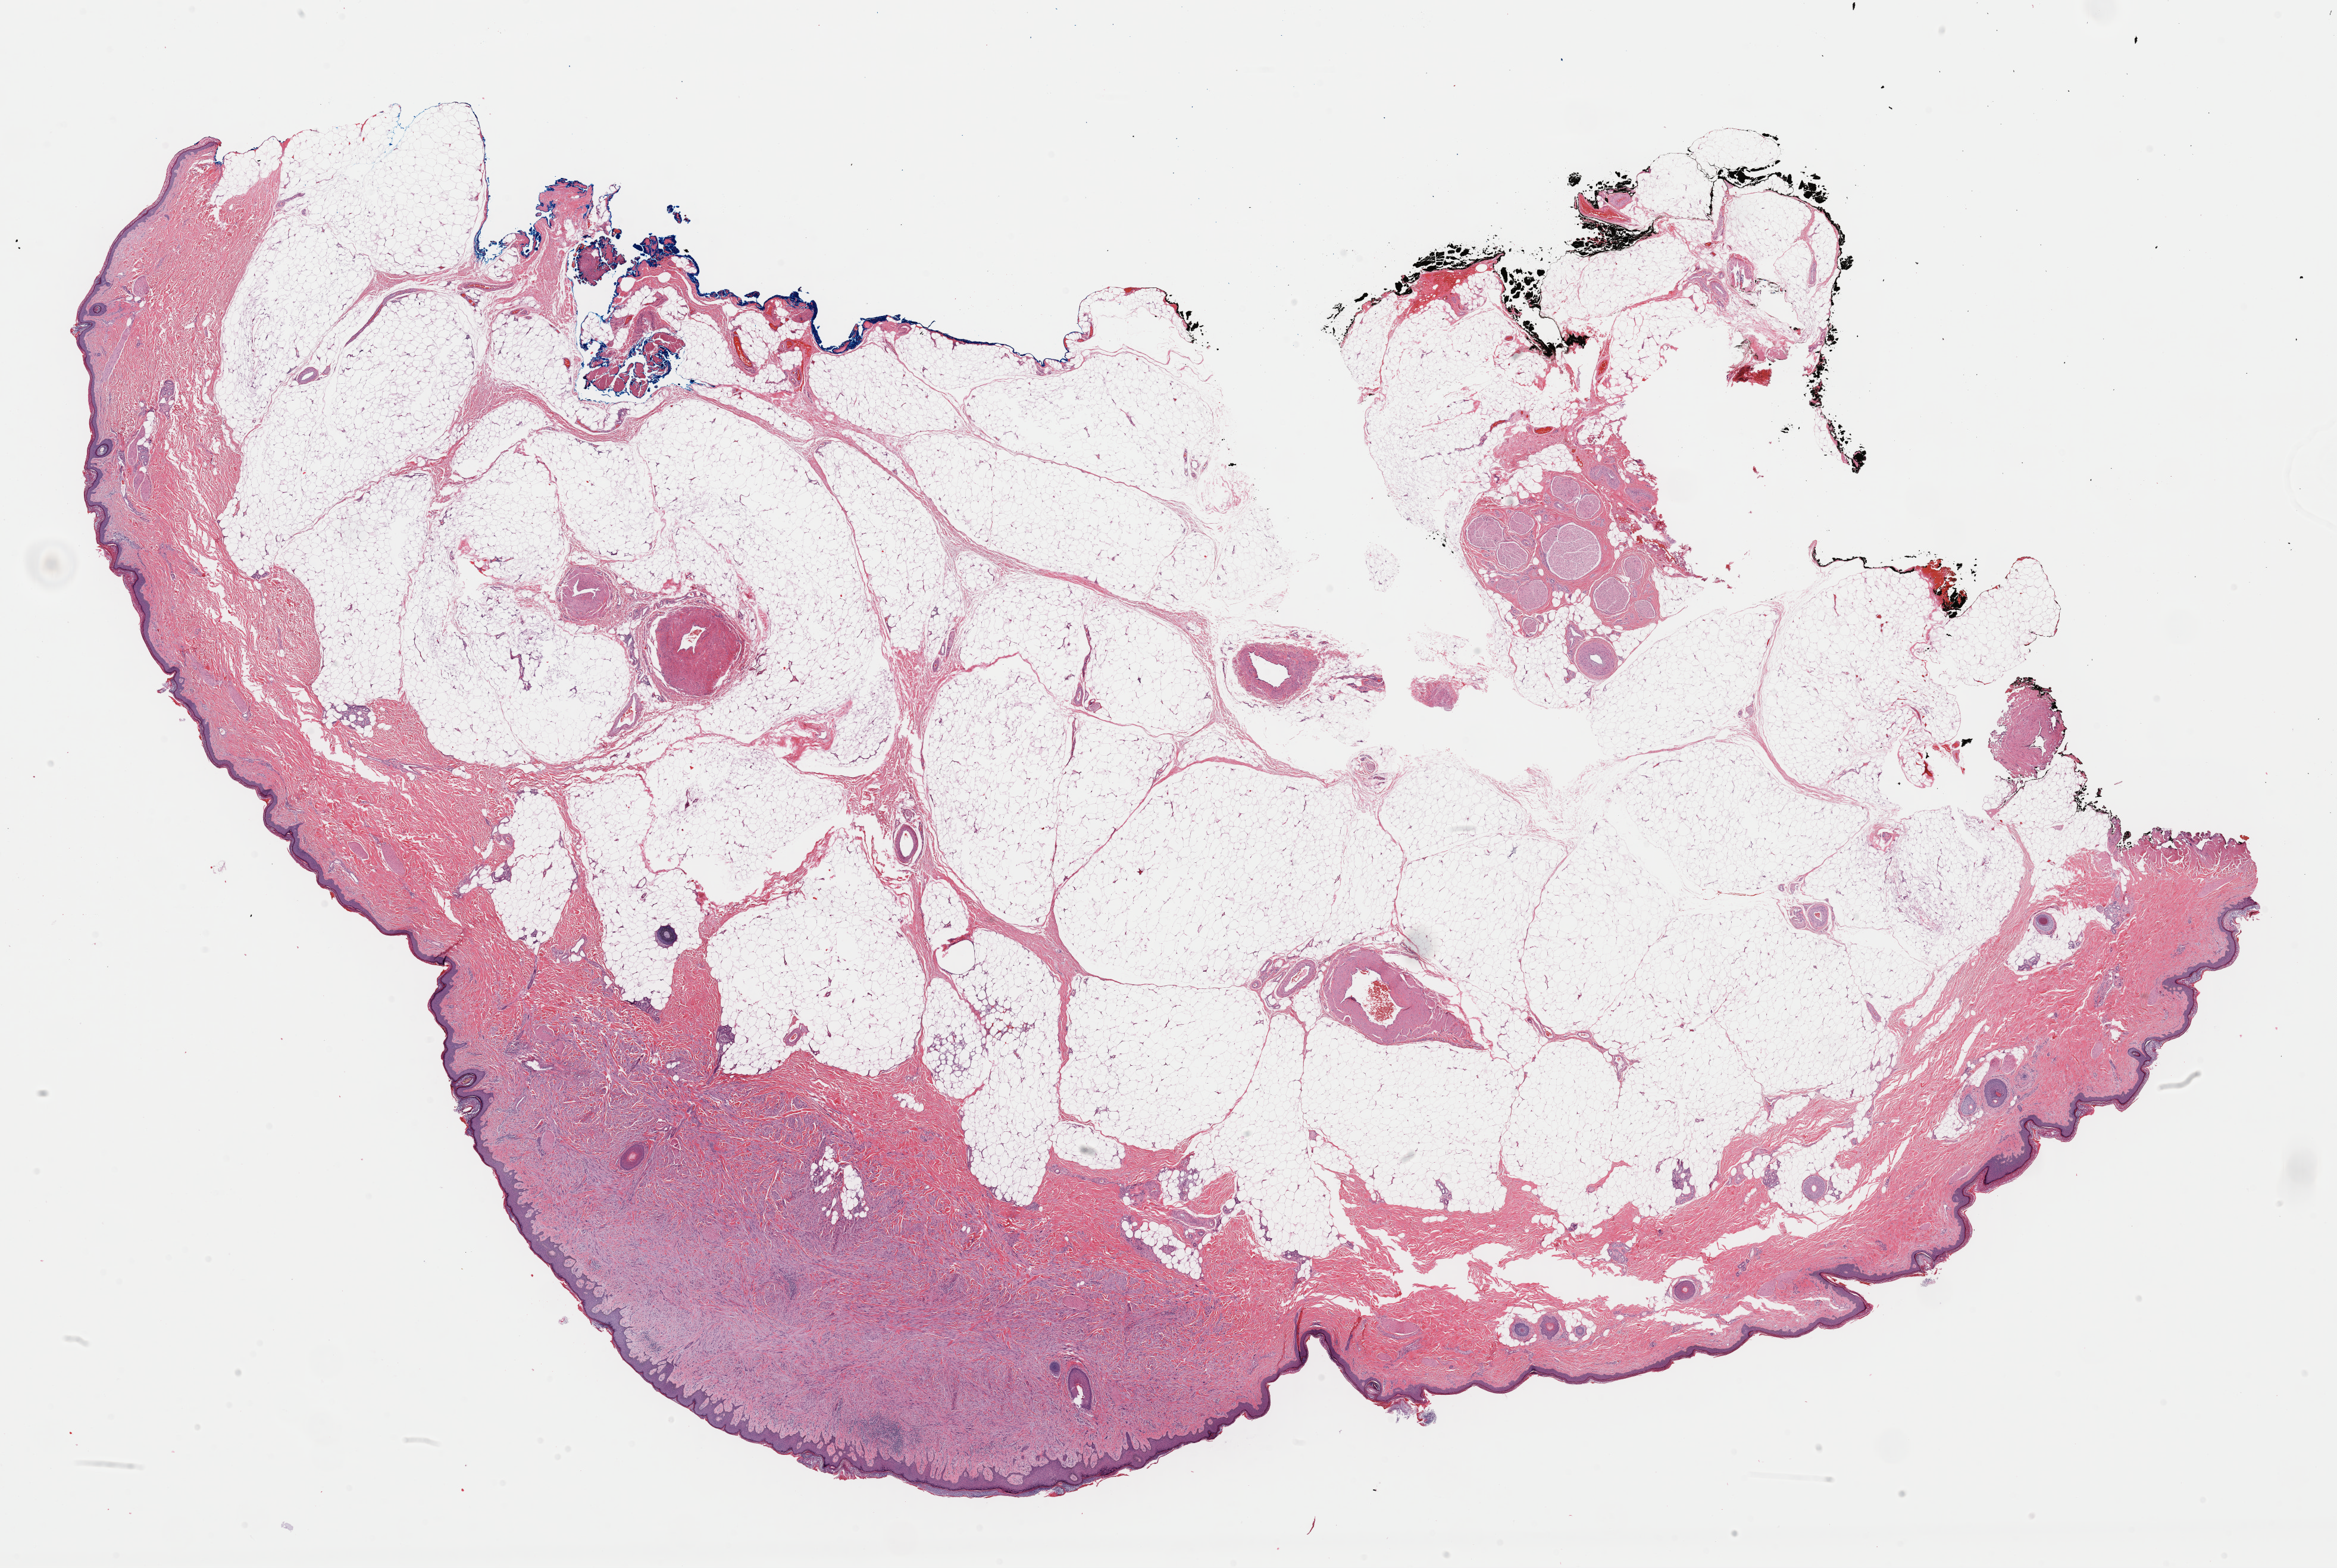
Digitized H&E tissue section (whole slide), a low-resolution overview of the entire scanned area, about 31.0 x 20.8 mm (slide scanned at 40x), formalin-fixed paraffin-embedded (FFPE) diagnostic section, primary tumour sample from the connective, subcutaneous and other soft tissues. Male patient; age at initial diagnosis 52 years.
Histologic diagnosis: Leiomyosarcoma, NOS.